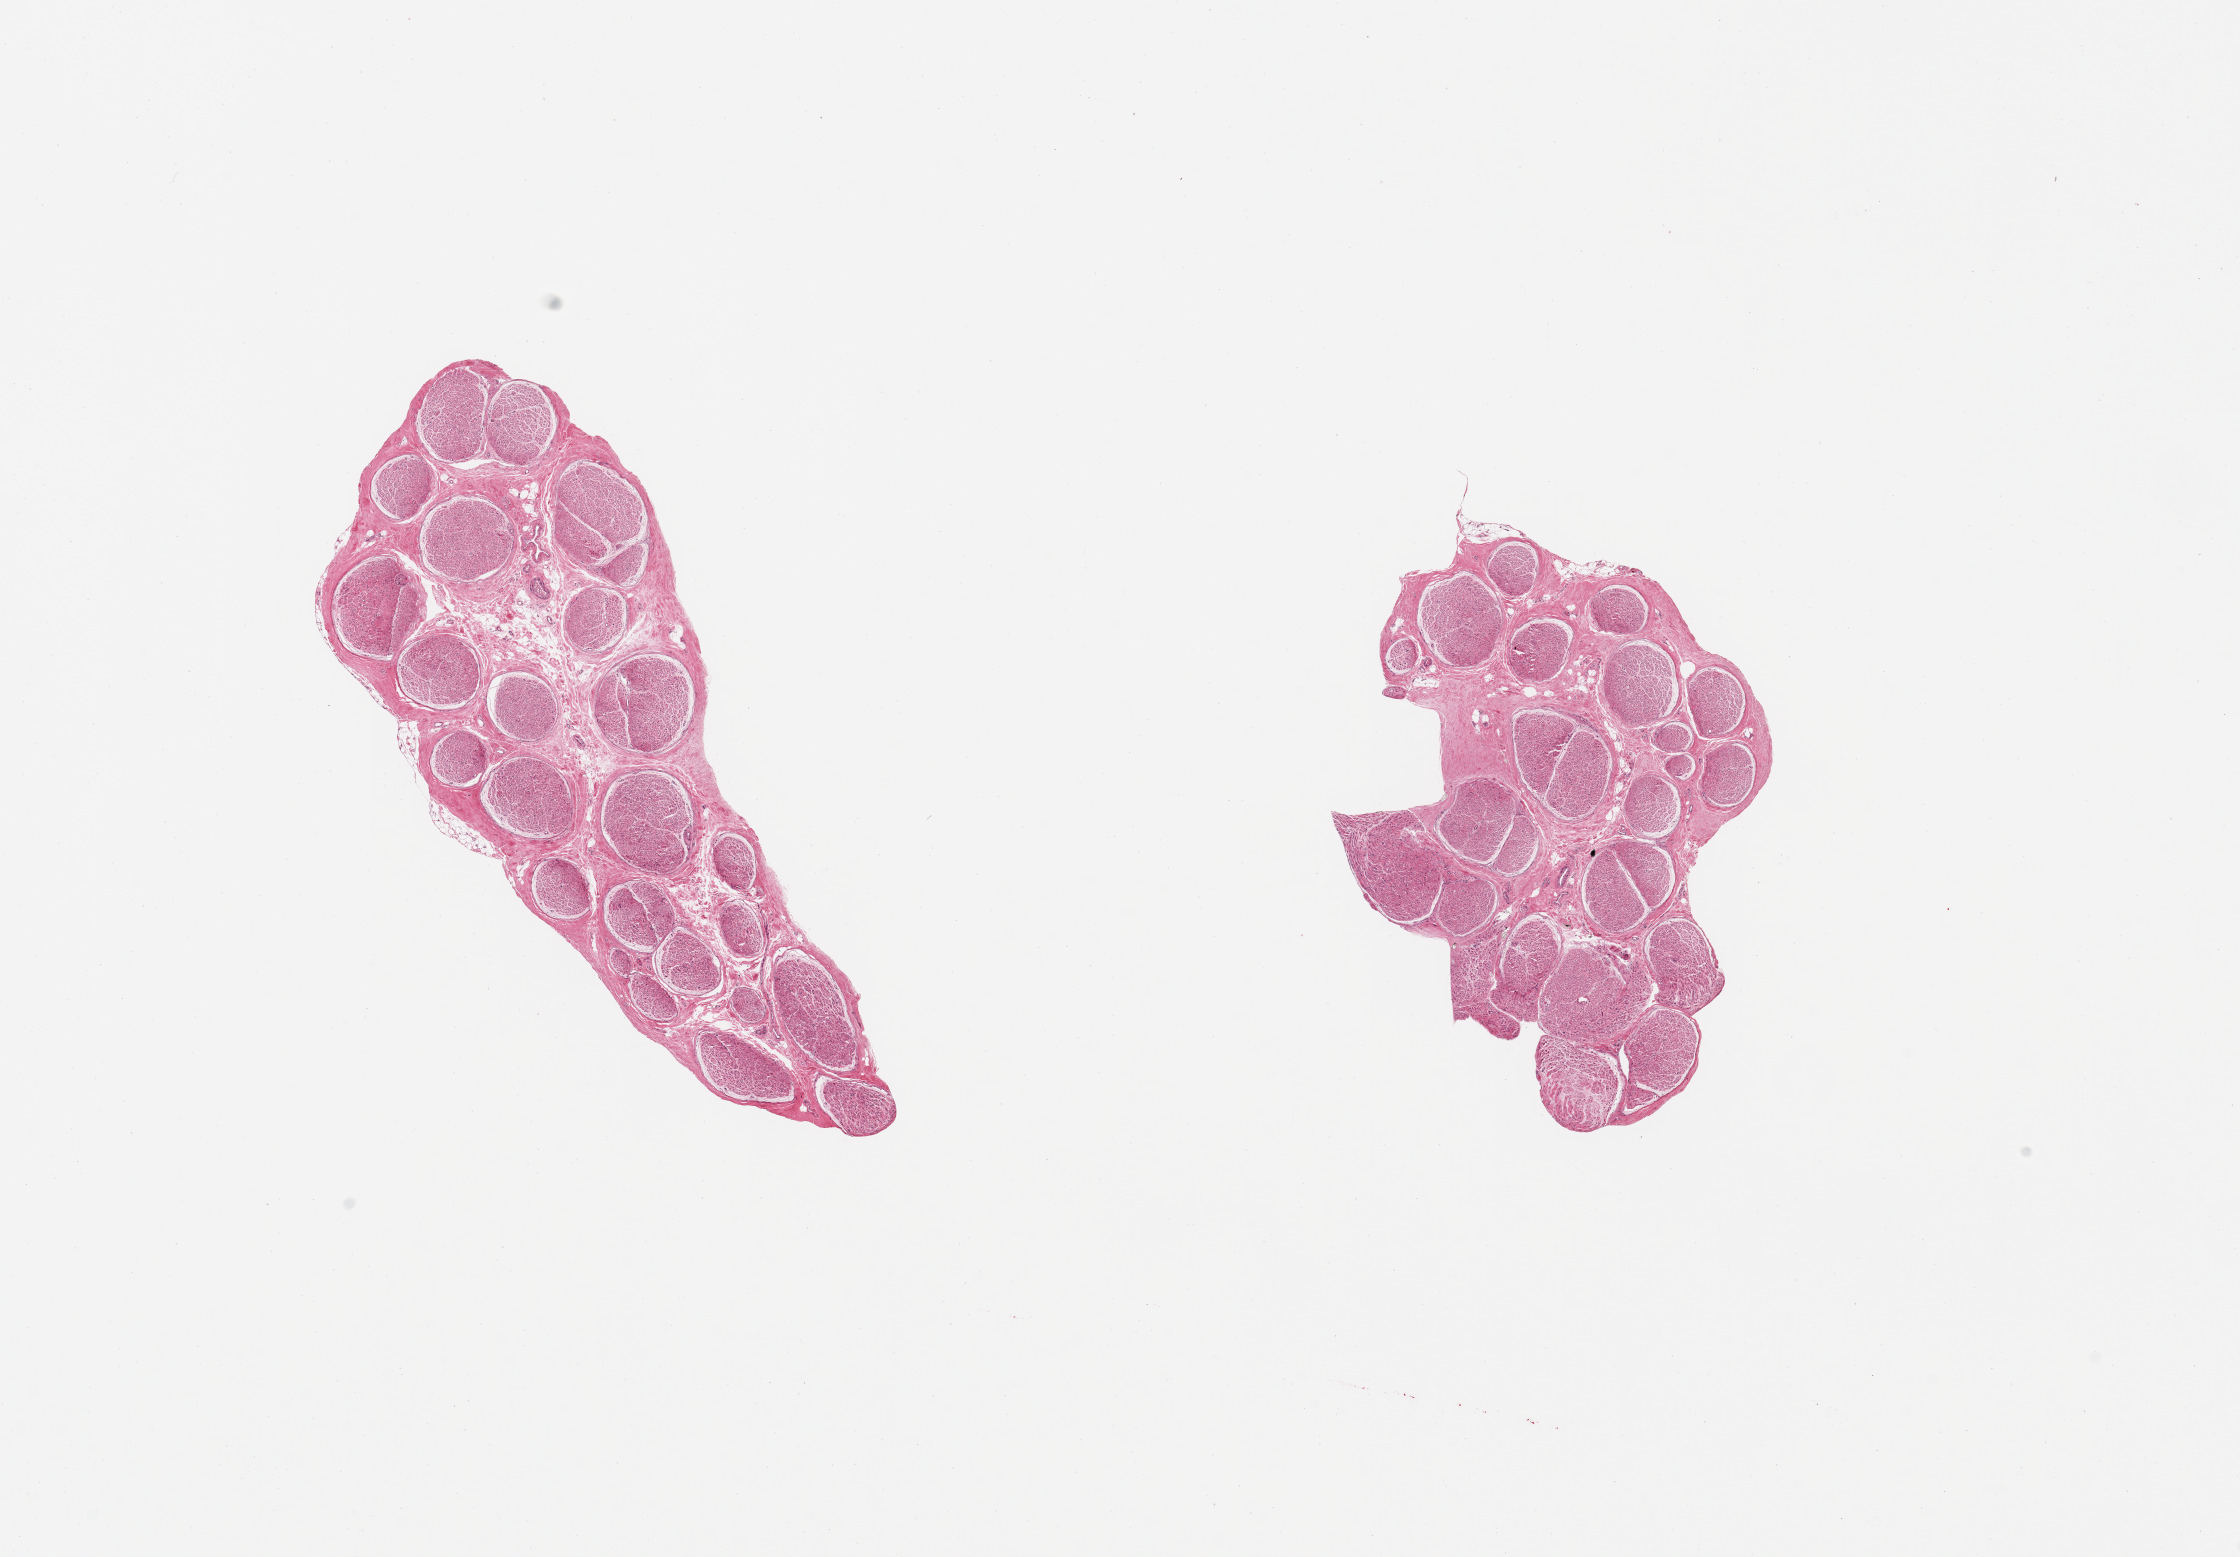
Digitized H&E-stained section — whole scanned area (about 17.7 x 12.3 mm, slide scanned at 20x) shown as a low-resolution overview. PAXgene-fixed, paraffin-embedded tissue. Sampled site (target tissue): tibial nerve. Donor tissue sample.
- pathologist's review note for this sample: 2 pieces; well dissected